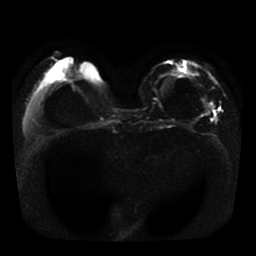
Breast MRI, one axial slice. Position 14 of 41 along the scan axis. Diffusion-weighted series; image 2 of 4 stored at this slice position (different b-values; order by instance number). 1.5 T. 5 mm slice thickness. 256 × 256 image matrix. Female patient.
Structures marked on this image (outlined manually by an expert reader):
- tumour on diffusion-weighted imaging: bounding box (x1, y1, x2, y2) in pixels: (200, 102, 215, 117)